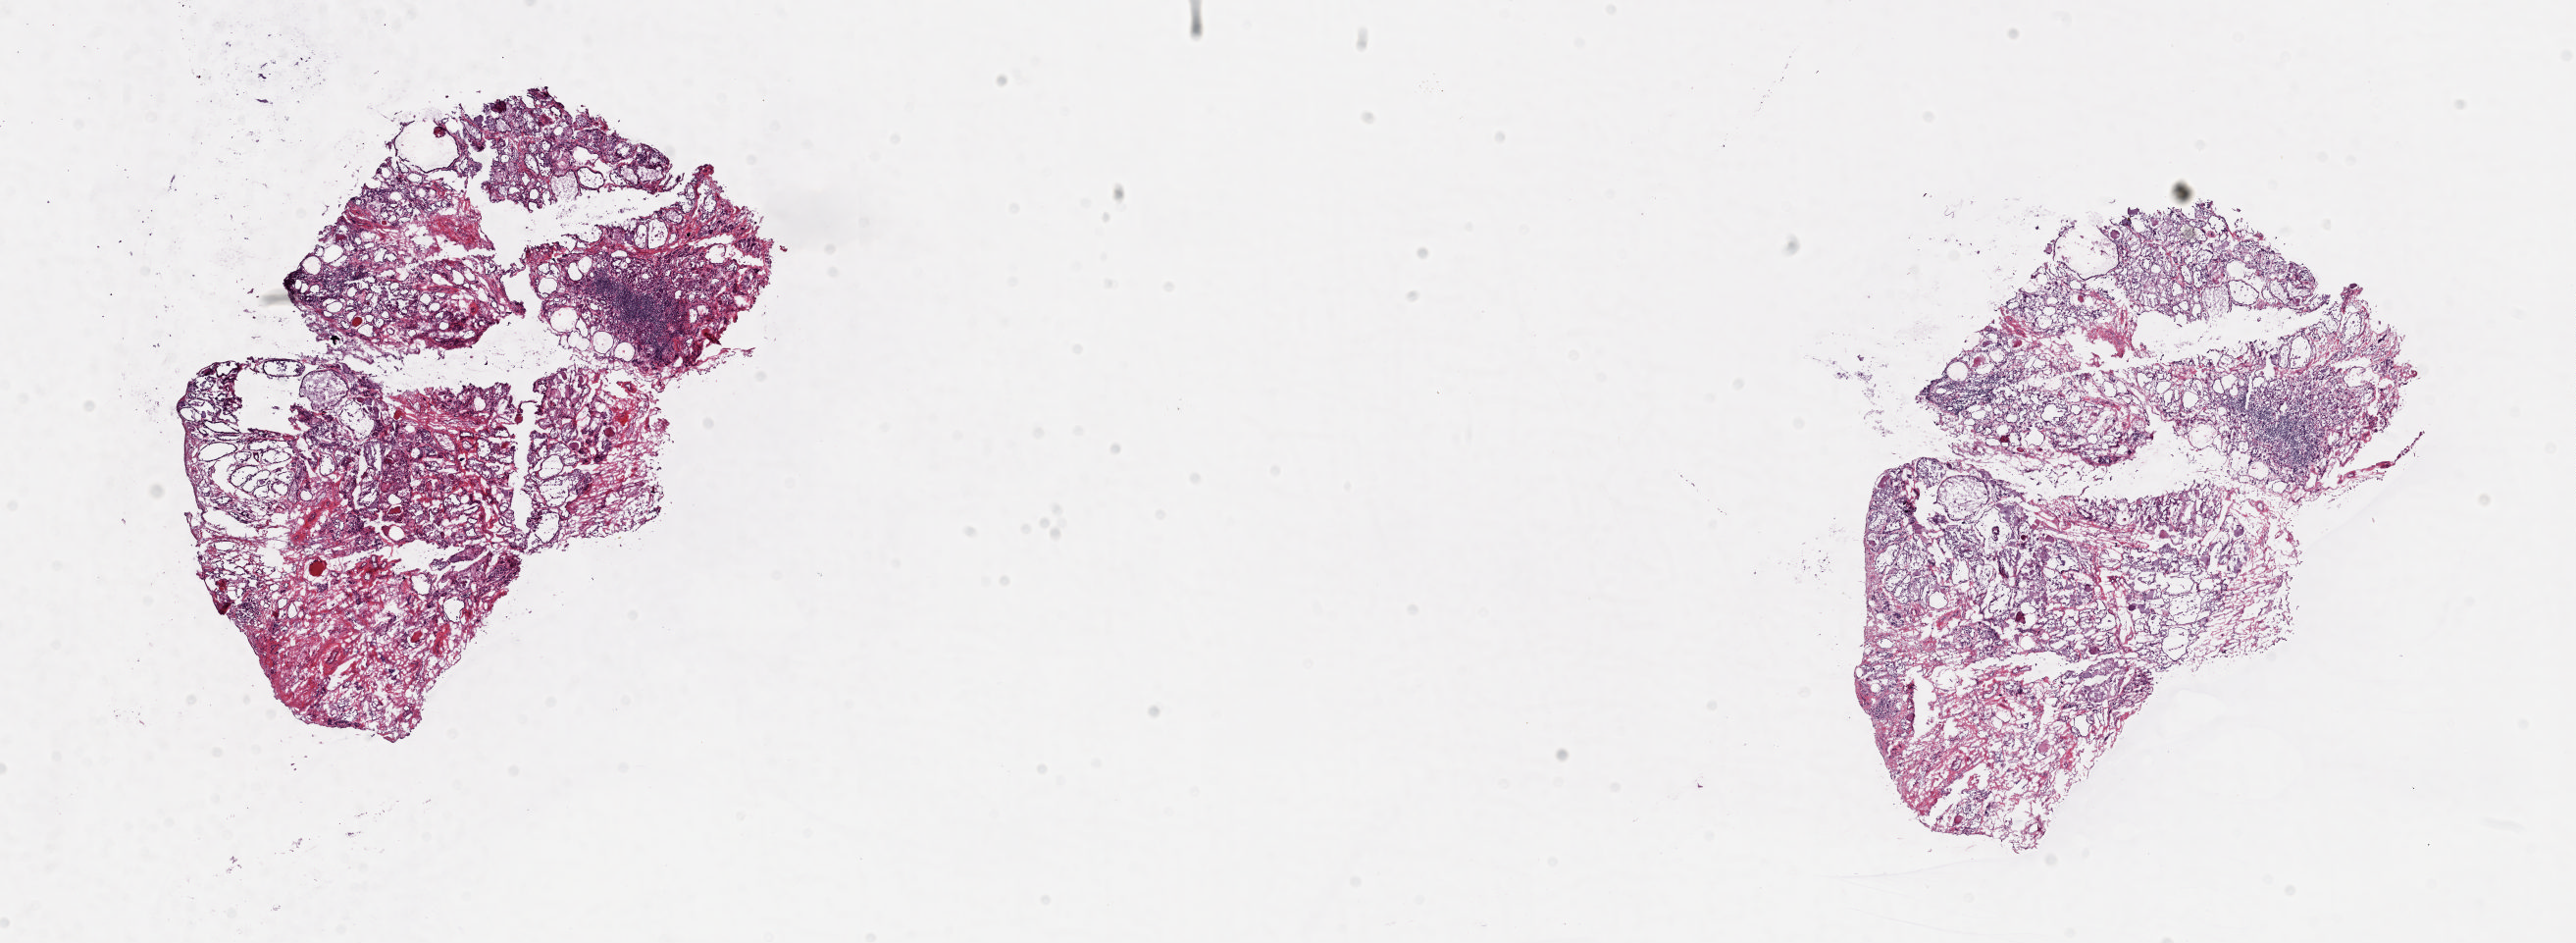
Digitized Hematoxylin and eosin (H&E) stained tissue section (whole slide) — low-resolution overview of the scanned area, about 20.8 x 7.6 mm; frozen section from the top of the tissue portion; solid tissue normal (non-tumour tissue) sample from the thyroid. Female, age 66 years at initial diagnosis. Pathologist review of this section (percent, as recorded): tumour cells 0%, tumour nuclei 0%, normal cells 100%, stromal cells 0%, necrosis 0%. Inflammatory infiltration, as recorded: lymphocyte infiltration 8%, monocyte infiltration 3%, neutrophil infiltration 0%.
* this section: solid tissue normal sample (biorepository sample class)
* patient diagnosis: Papillary adenocarcinoma, NOS (thyroid gland)